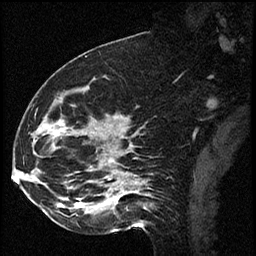
Breast MRI (dynamic contrast-enhanced), one sagittal slice. Position 27 of 60 along the scan axis. Dynamic contrast-enhanced series, image 2 of 2 at this slice position (ordered by acquisition). 1.5 T. TE 4.2 ms, TR 17.3 ms. 2 mm slice thickness. 256 × 256 image matrix, field of view 200 × 200 mm. Female patient. Case-level facts recorded for this patient, not image findings: setting: breast cancer imaged before/during neoadjuvant chemotherapy; receptor status: HR-positive, HER2-negative.
Structures marked on this image (semi-automatically segmented with operator editing):
- analysis volume of interest (the breast-tissue region the enhancement analysis was run in; not a lesion): bounding box <41,93,115,223> (left, top, right, bottom; pixels)
- tumour enhancement mask (voxels above the 100 % enhancement threshold inside the analysis volume of interest): <78,203,82,206>